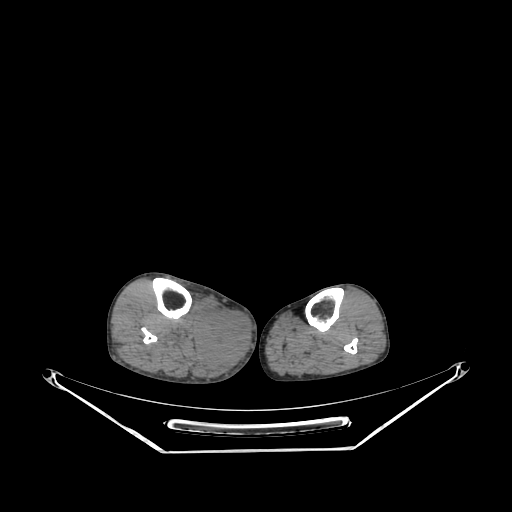
CT of an extremity soft-tissue mass (from a PET/CT study), one axial slice. Reconstruction kernel SOFT. 140 kVp. Soft-tissue window (W 400 / L 40 HU). 3.75 mm slice thickness. 512 × 512 image matrix. Male patient. From the clinical record (not read from this slice): histological type: pleiomorphic liposarcoma; grade: high; site of the primary tumour: right calf.
Structures marked on this image (expert contour drawn on MRI and transferred to this co-registered scan by the dataset authors):
- gross tumour volume including surrounding oedema: bounding box (x1, y1, x2, y2) in pixels: (196, 306, 248, 366)
- gross tumour volume (mass): (196, 311, 250, 364)